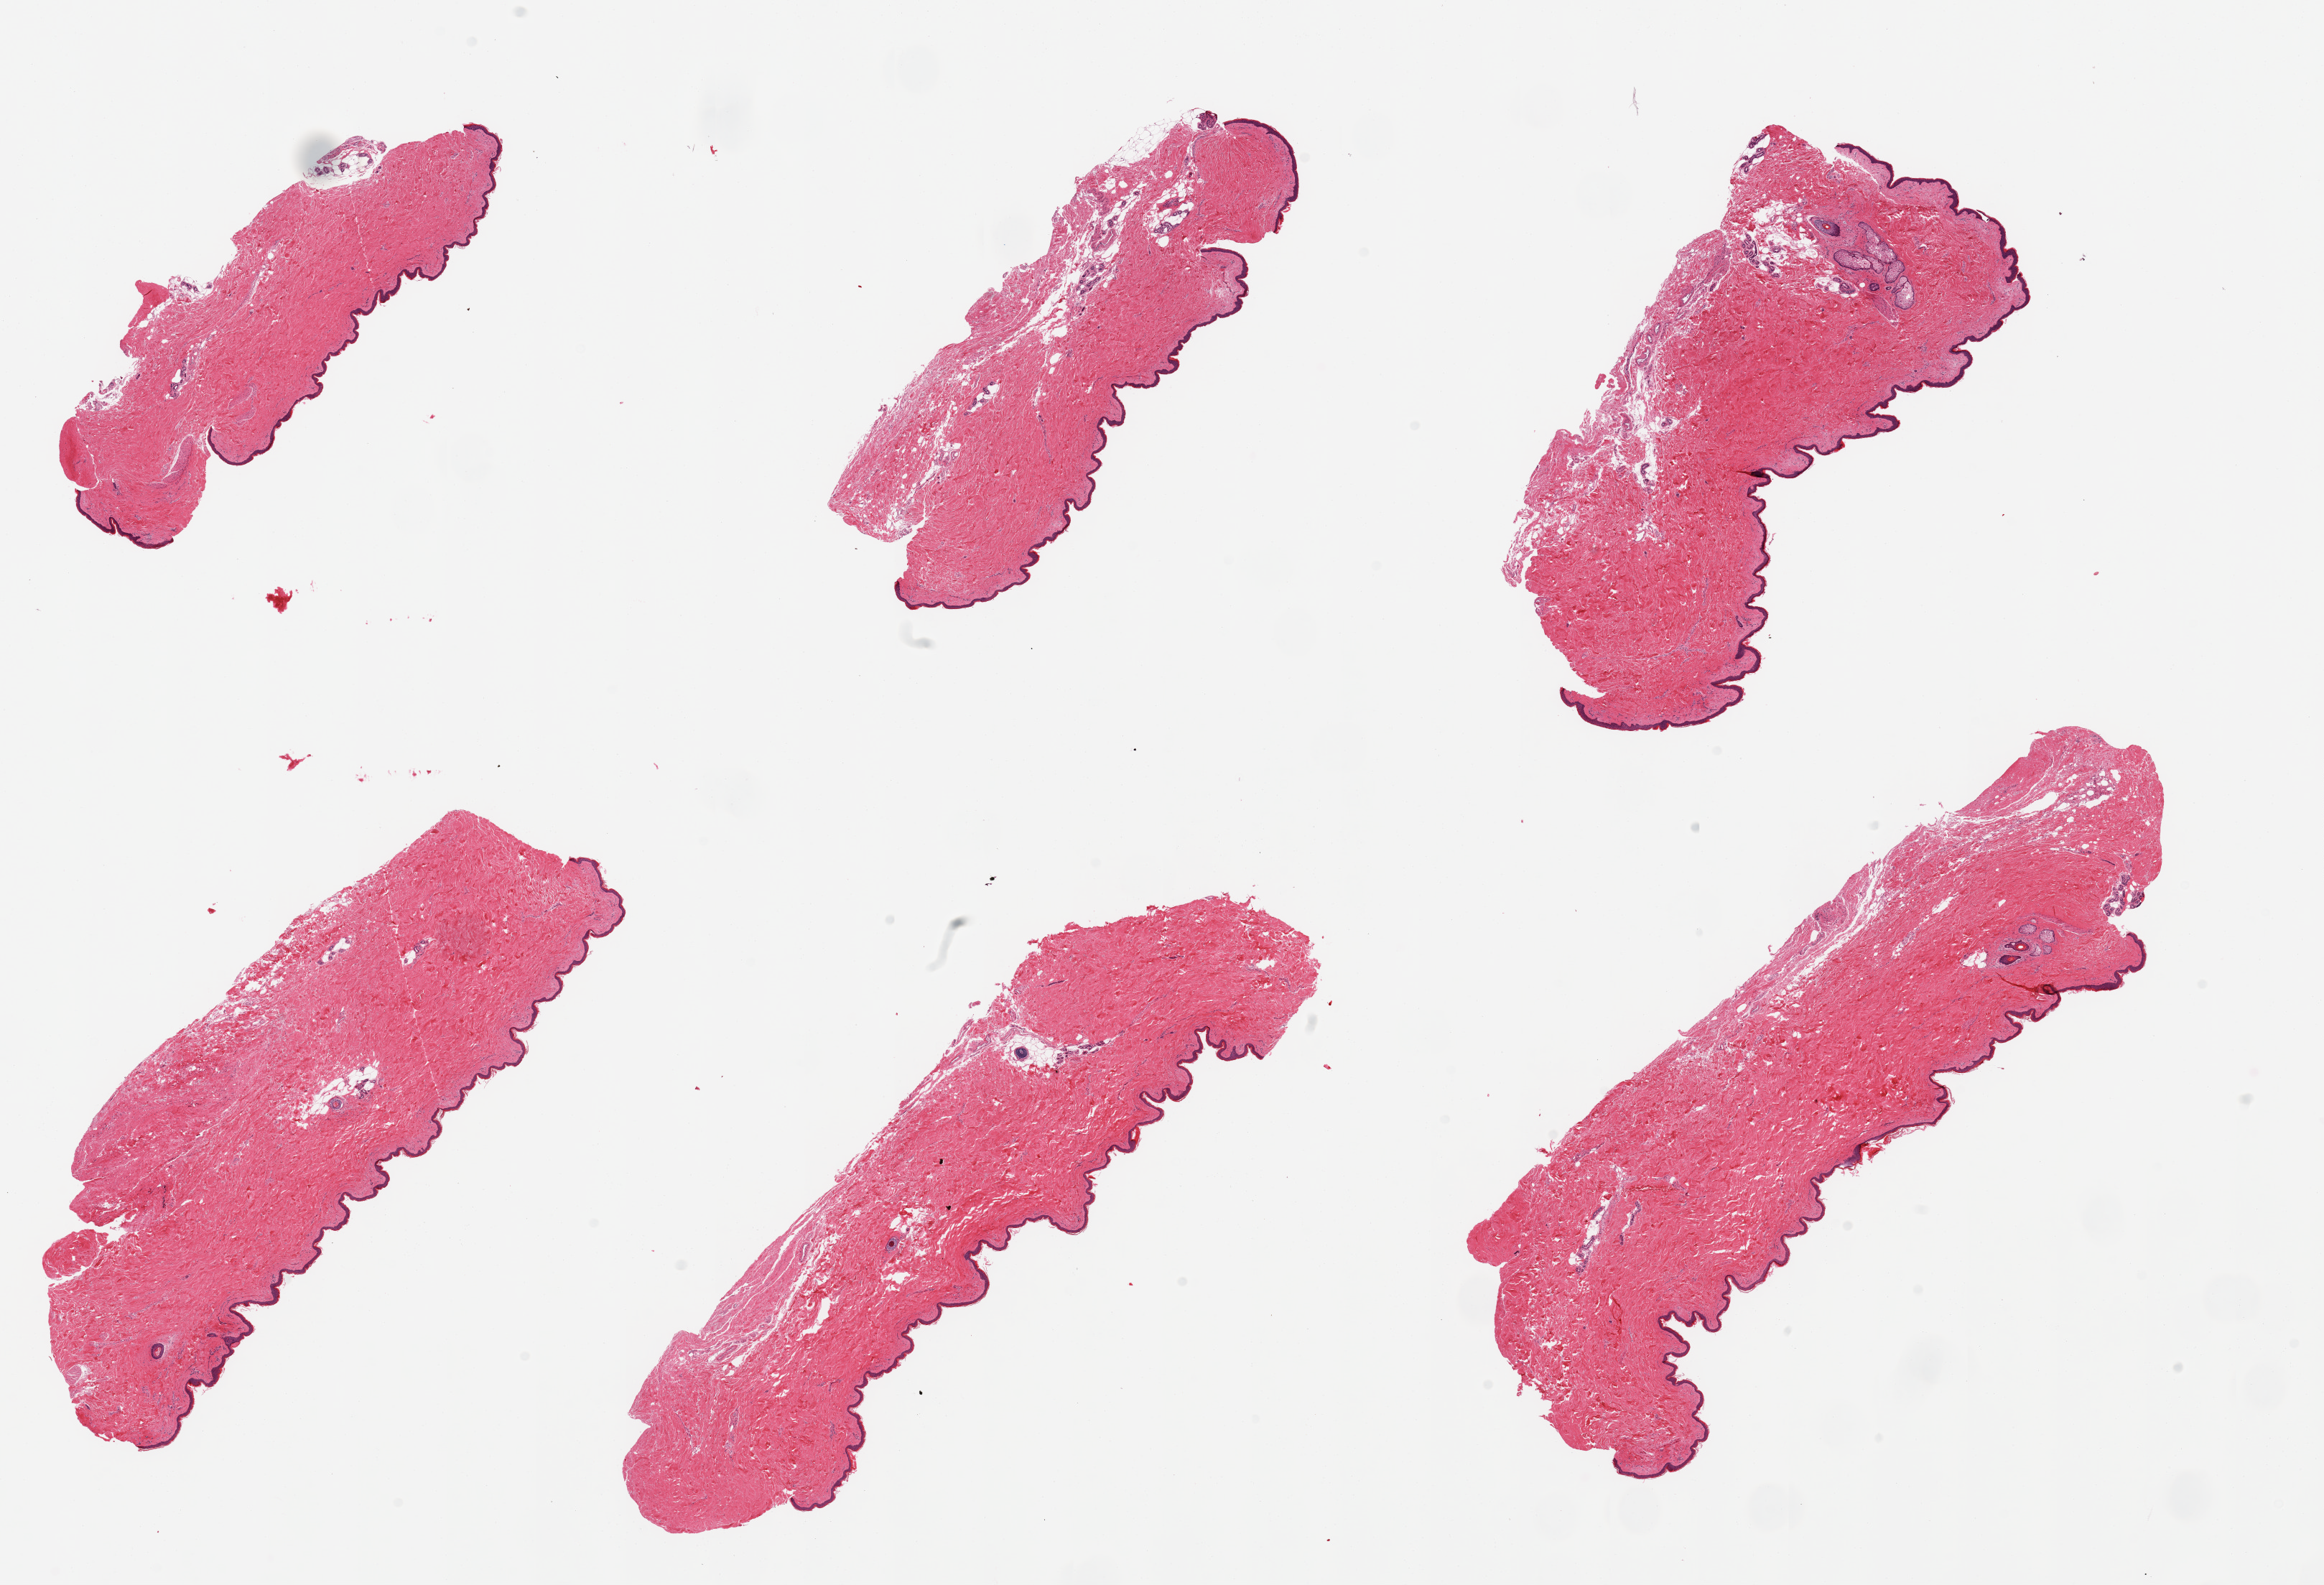
Digitized hematoxylin and eosin (H&E)-stained section, brightfield — whole scanned area (about 25.6 x 17.5 mm, acquisition: 20x scan) shown as a low-resolution overview; PAXgene-fixed, paraffin-embedded tissue; target tissue: skin of suprapubic region; donor tissue sample.
Reviewer comment on this tissue sample: 6 pieces; well trimmed, up to 10% internal fat.